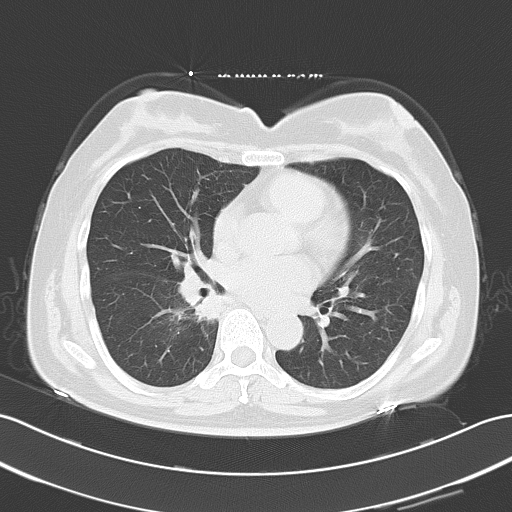
Chest CT, one axial slice. Position 28 of 55 along the scan axis. Reconstruction kernel B70f. 120 kVp. Lung window (W 1500 / L -600 HU). 5 mm slice thickness. 512 × 512 image matrix, field of view 353 × 353 mm. Female patient, age 59 years. Case-level facts recorded for this patient, not image findings: clinical TNM (as recorded): T1c N0 M1b.
Annotated regions visible in this slice (rectangle marked by the reading radiologist):
- lung tumour (recorded histology: adenocarcinoma): box from (x=175, y=284) to (x=221, y=324) px